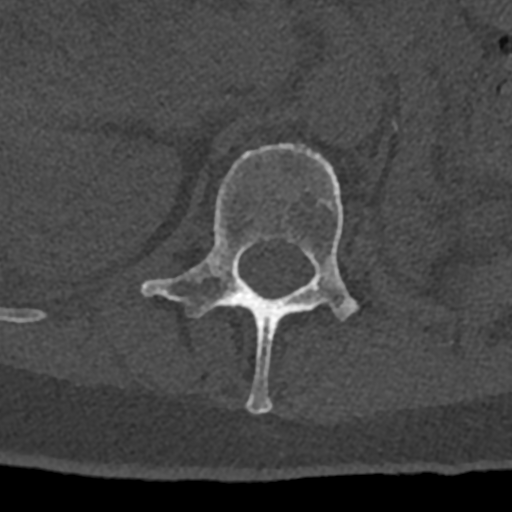
CT including the spine, one axial slice; position 438 of 797 along the scan axis; reconstruction kernel Br40s/3; 120 kVp; bone window (W 1800 / L 400 HU); 0.5 mm slice thickness; 512 × 512 image matrix, field of view 160 × 160 mm. Male patient, age 74 years. Case-level facts recorded for this patient, not image findings: primary cancer: renal.
Annotated regions visible in this slice (semi-automatically segmented with operator editing):
- L1 vertebra: bounding box <141,143,358,414> (left, top, right, bottom; pixels)